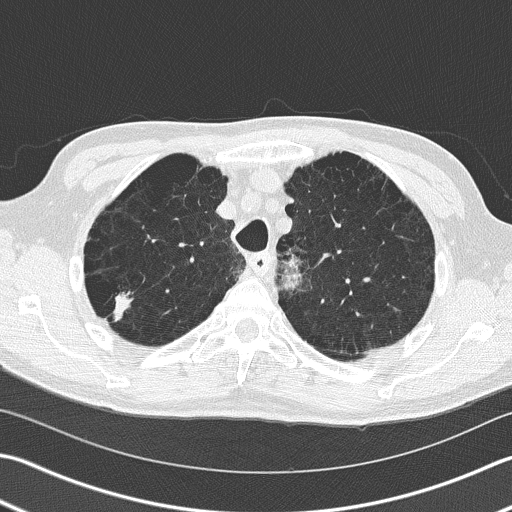
Axial slice from a low-dose chest CT screening exam, first (baseline) screen, lung window (W 1500 / L -600 HU), lung (sharp) reconstruction kernel (B50f), slice 39 of 163 in the series. Male, age 66 years at enrolment. Current smoker at enrolment.
Expert reader's lesion annotation, bounding box [x1, y1, x2, y2] px = [88, 272, 146, 339]. Screening reader's record for this exam (one nodule recorded; not confirmed to be the boxed lesion): non-calcified nodule or mass ≥4 mm, right upper lobe, 39 × 23 mm, spiculated (stellate) margins, soft tissue attenuation. Later outcome: lung cancer diagnosed 36 days after this screen — squamous cell carcinoma, NOS, right upper lobe, poorly differentiated (G3), stage IB (AJCC 6th edition), 23 mm at pathology.